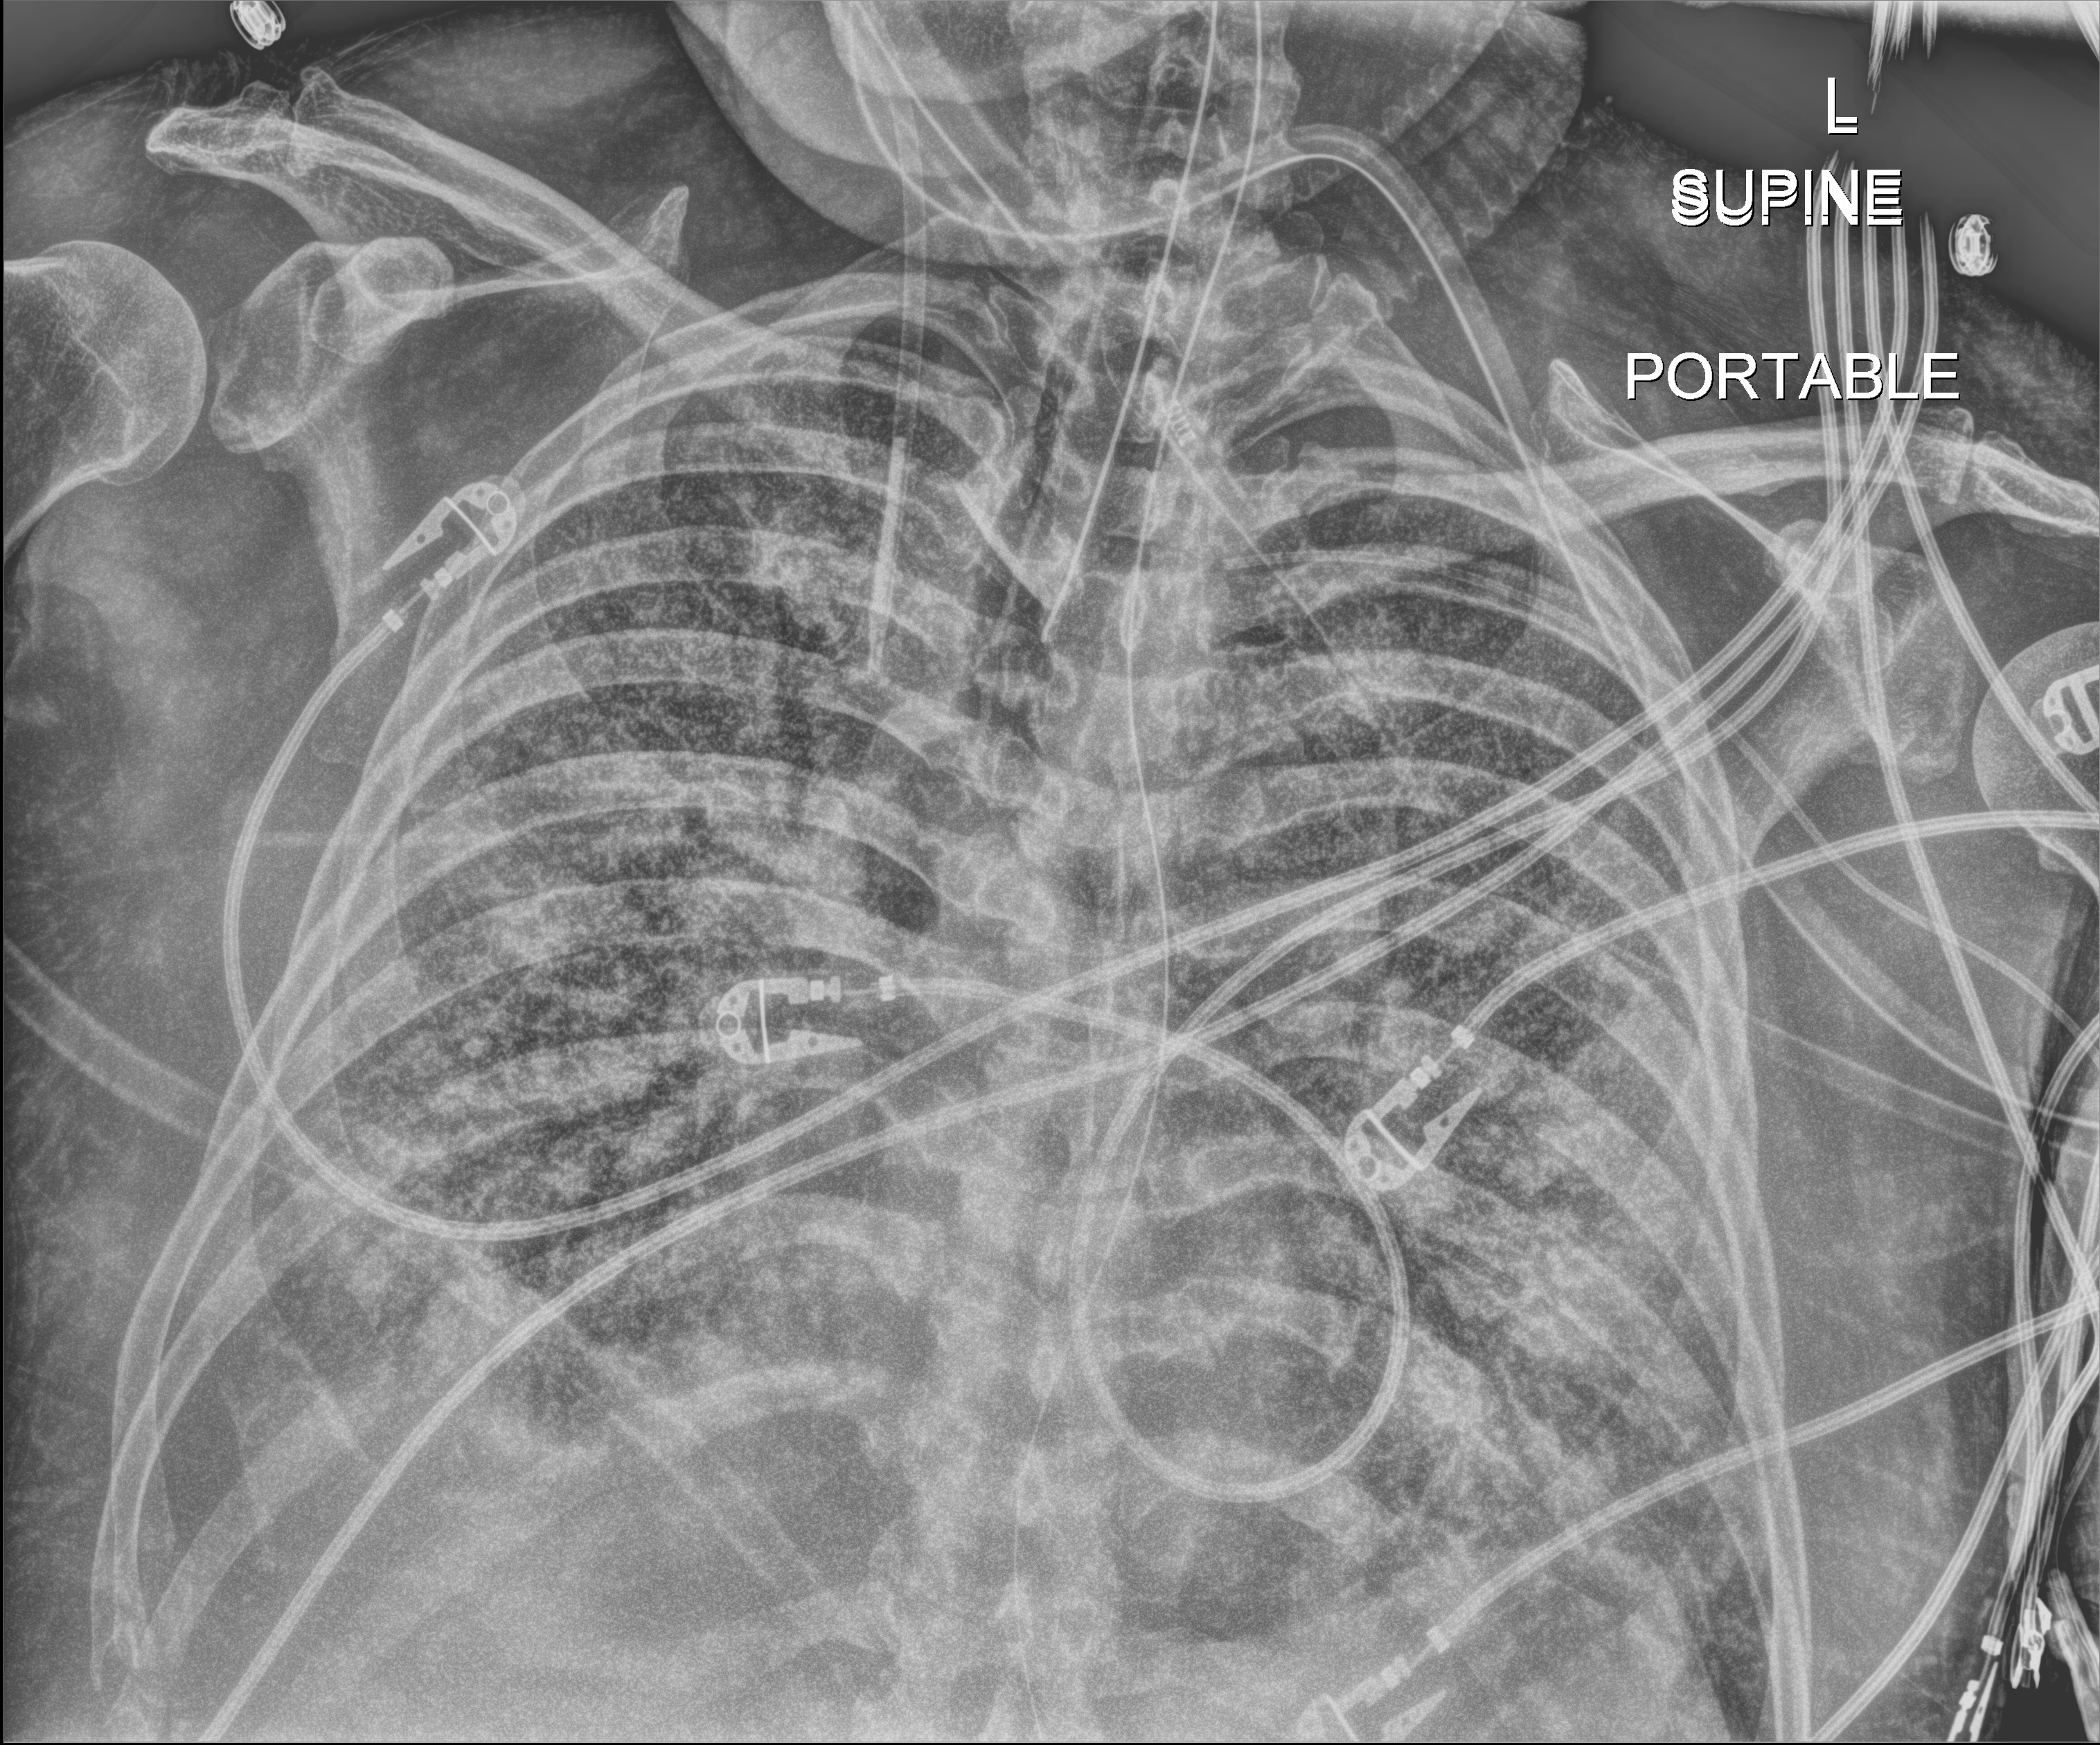
Bedside chest radiograph (digital radiography); anteroposterior (AP) projection. Male patient hospitalised with COVID-19, age 60–74 years.
Hospital-stay facts (about this admission, not read from this image; timing relative to this image not recorded): smoking status (admission record): never; COPD (admission record): no.